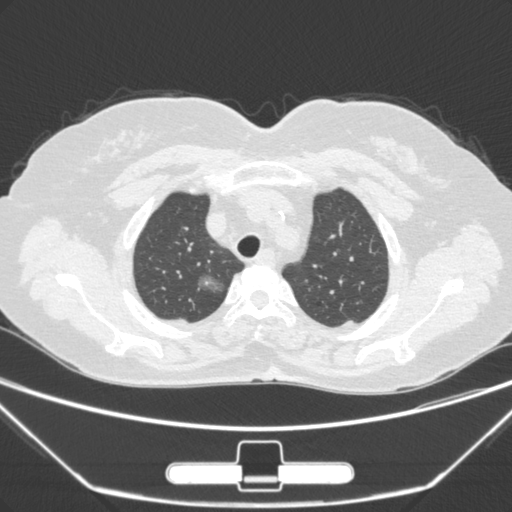
Chest CT, one axial slice; position 230 of 275 along the scan axis; 120 kVp; lung window (W 1500 / L -600 HU); 1 mm slice thickness; 512 × 512 image matrix, field of view 356 × 356 mm. Patient: female, 63 years. From the clinical record (not read from this slice): clinical TNM (as recorded): T1a N0 M0.
Structures marked on this image (rectangle marked by the reading radiologist):
- lung tumour (recorded histology: adenocarcinoma): bounding box <187,264,230,306> (left, top, right, bottom; pixels)